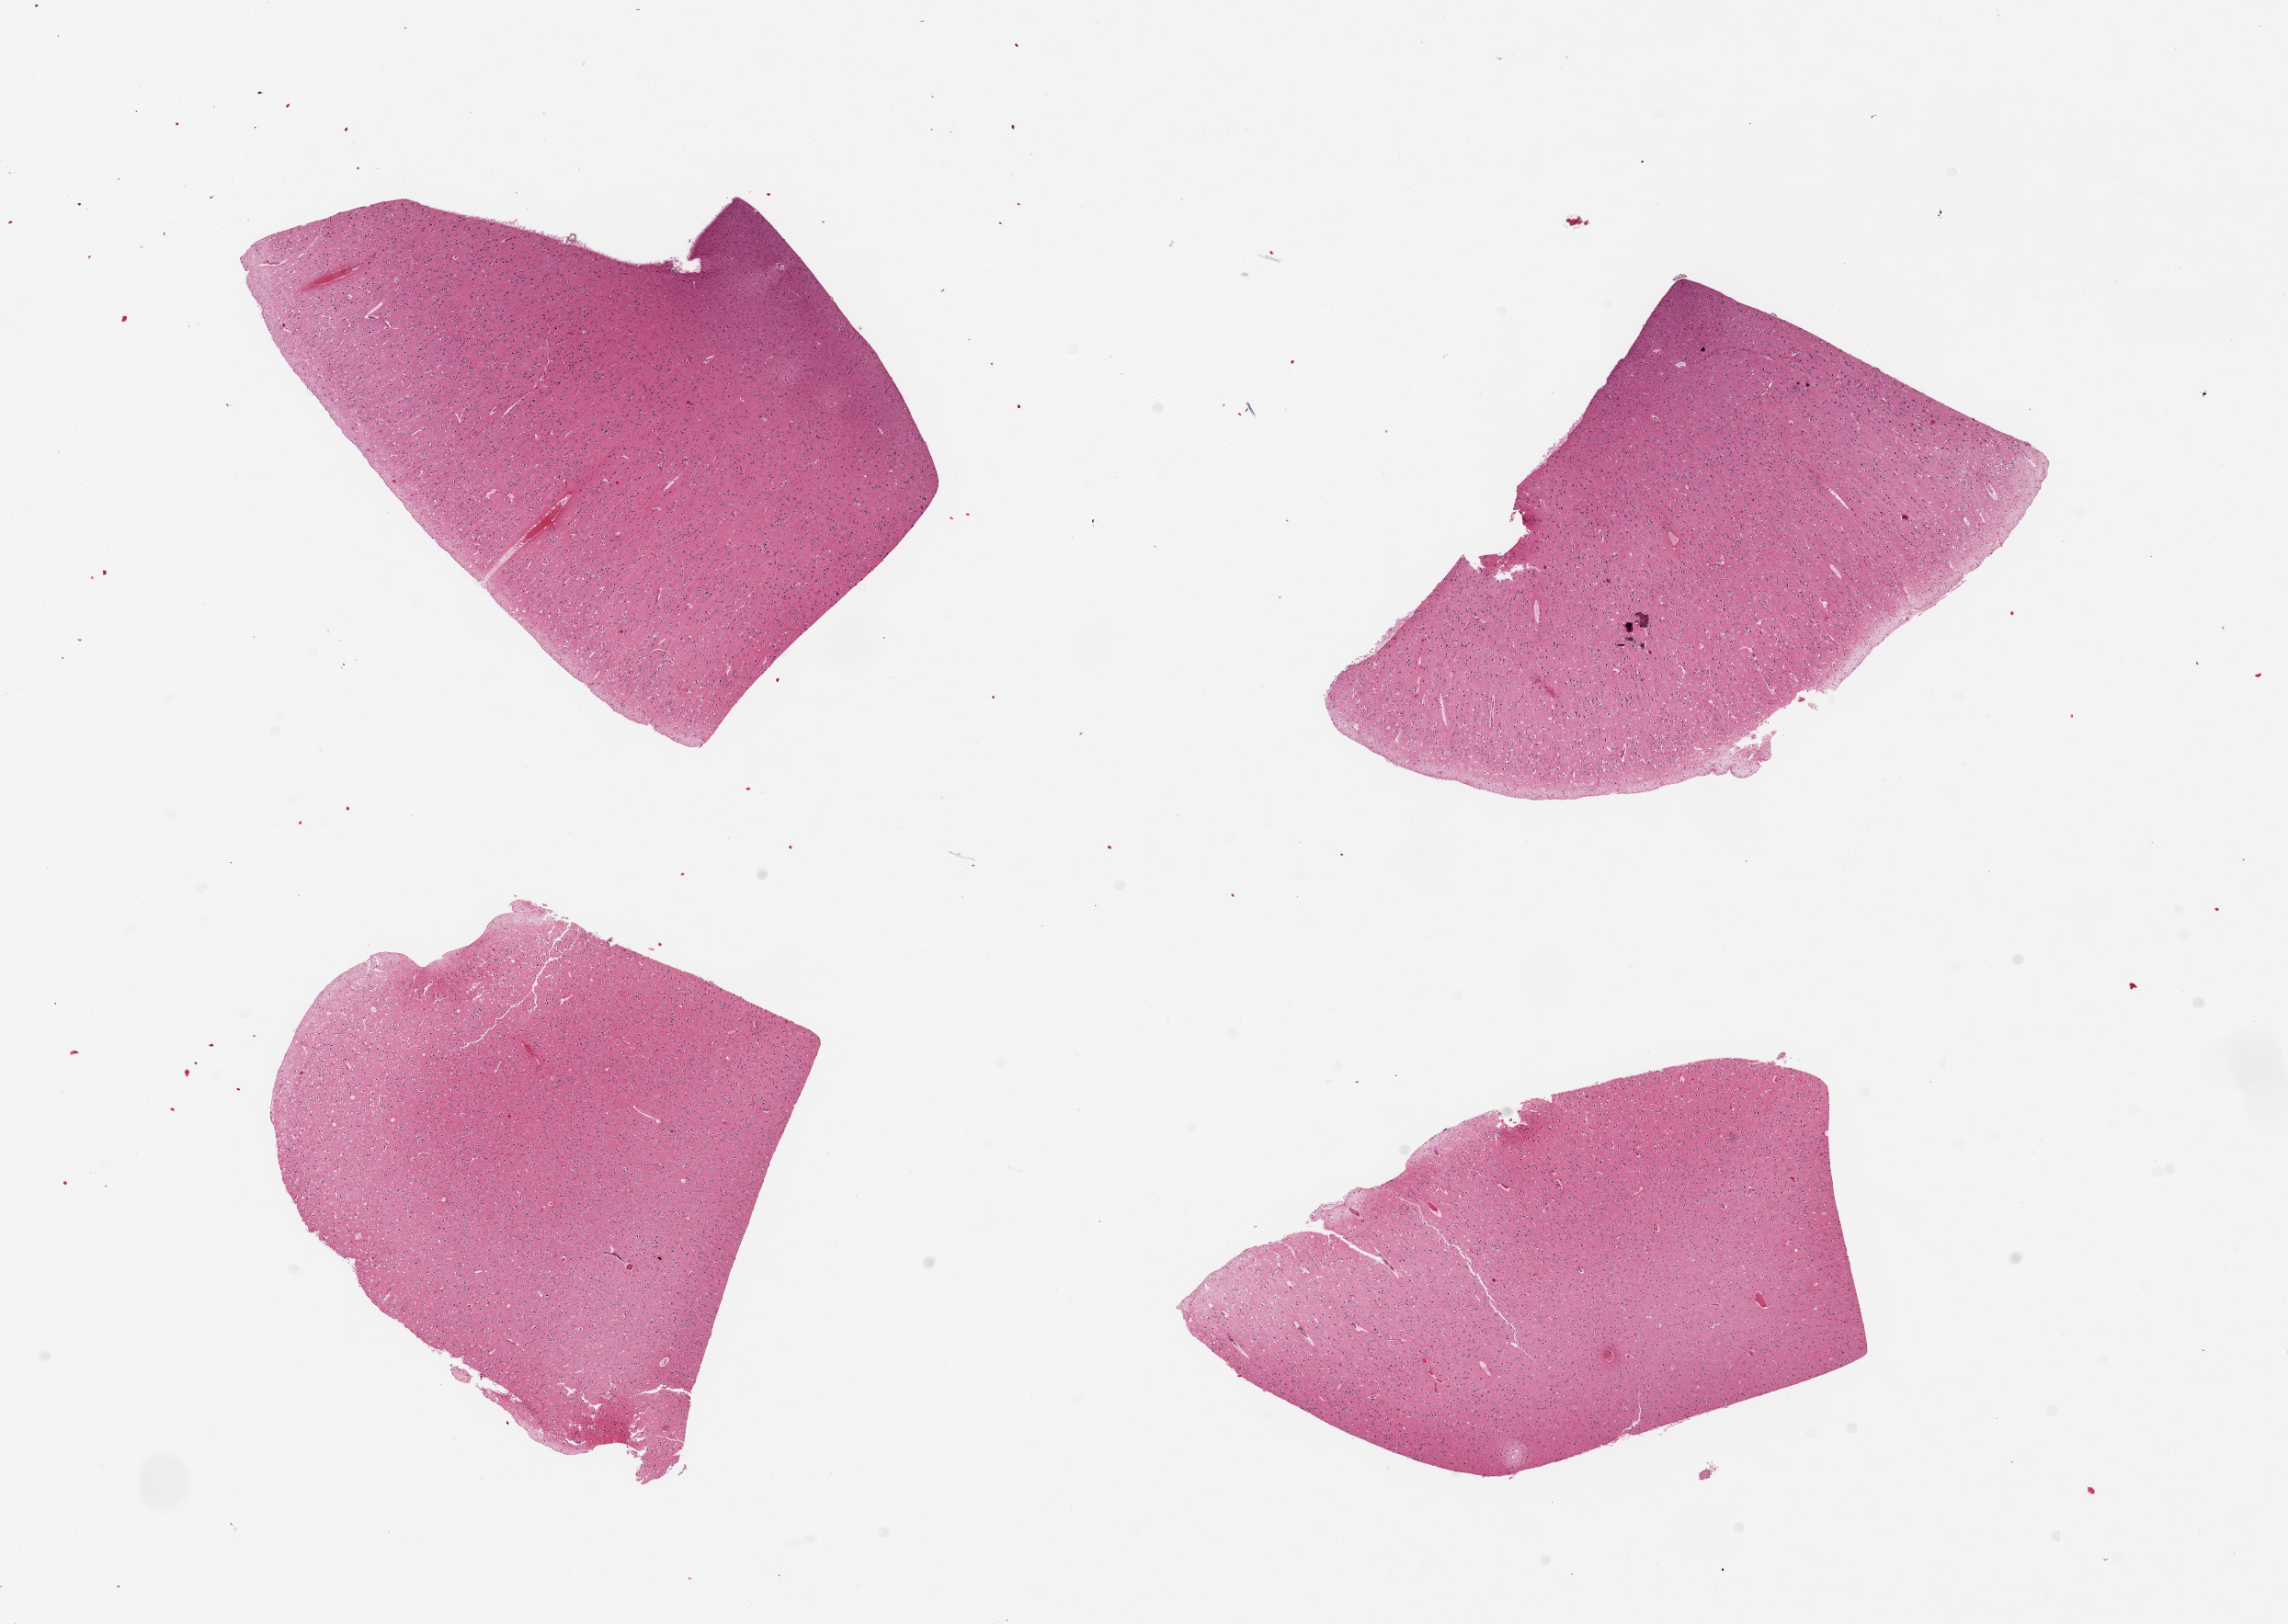
Whole-slide image, H&E stain, brightfield, low-resolution overview of the scanned area, about 19.7 x 14.0 mm (from a 20x scan). PAXgene-fixed paraffin-embedded (PFPE) section. Sampled site (target tissue): cerebral cortex. Tissue donor sample. Donor: male.
Pathologist's review note for this sample: 4 pieces, no abnormalities.